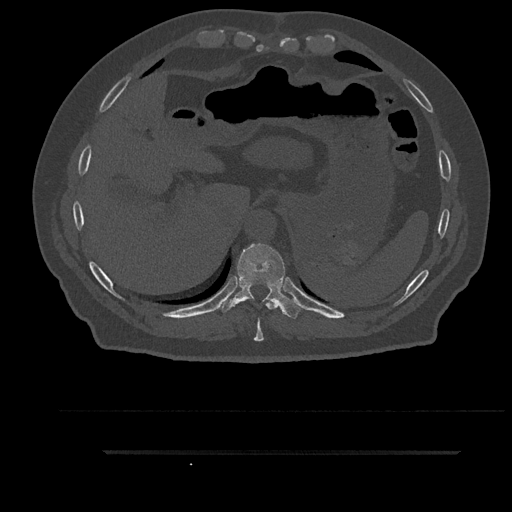
CT including the spine, one axial slice. Slice 387 of 797 in the series (ordered by position). Reconstruction kernel Br40s/3. Bone window (W 1800 / L 400 HU). 0.5 mm slice thickness. 512 × 512 image matrix. Patient: male, 63 years. From the clinical record (not read from this slice): primary cancer: renal.
Structures marked on this image (semi-automatically segmented with operator editing):
- T10 vertebra: bounding box <221,244,302,319> (left, top, right, bottom; pixels)
- T9 vertebra: <254,299,278,341>